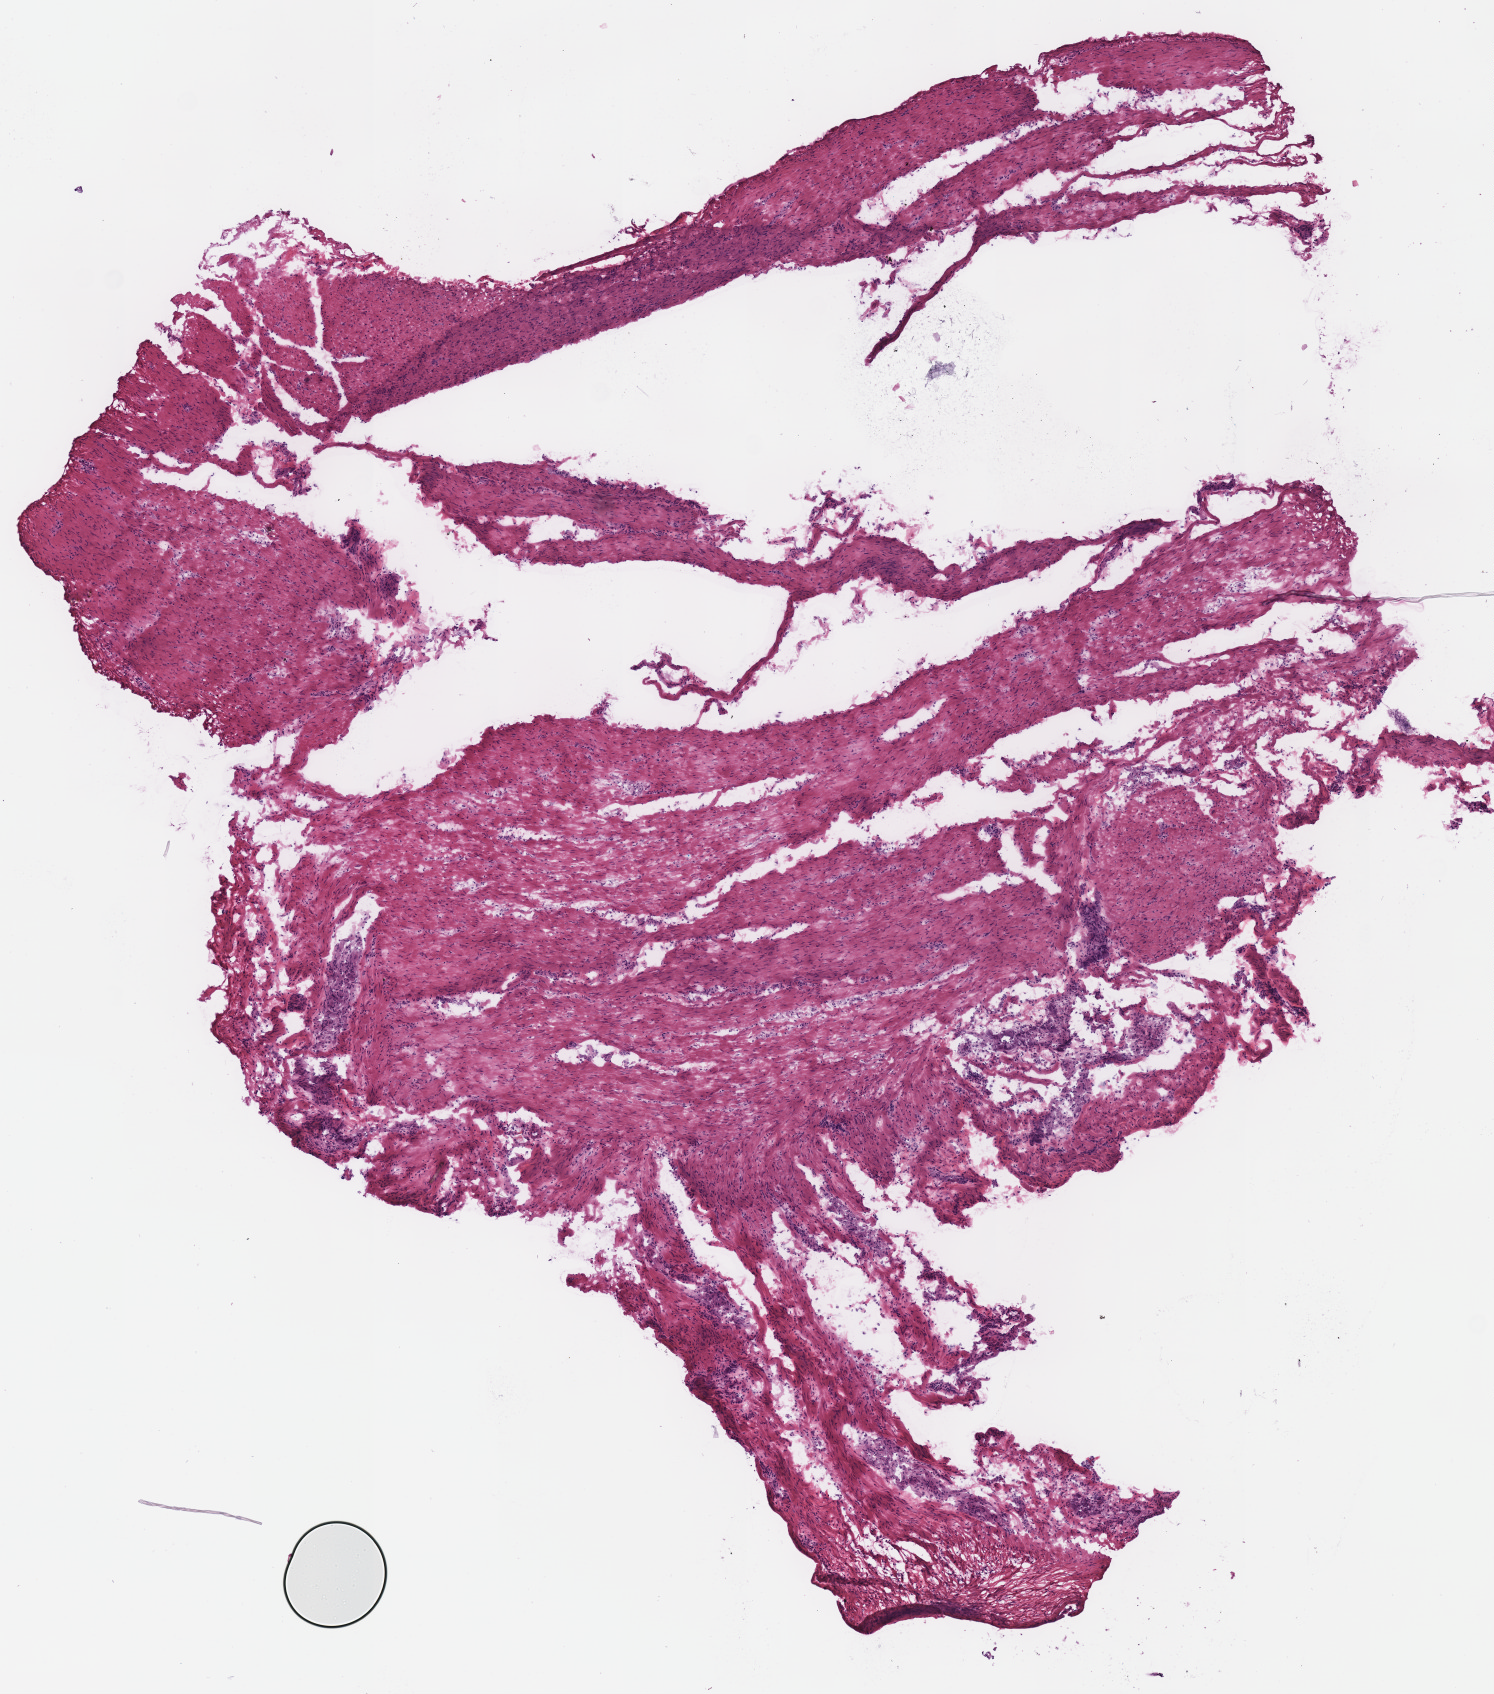
Hematoxylin and eosin (H&E) stained whole-slide image — low-resolution overview of the scanned area, about 5.9 x 6.7 mm (acquisition: 40x scan), frozen section from the top of the tissue portion, solid tissue normal (non-tumour tissue) sample from the stomach. Patient: male, age at initial diagnosis 75 years.
This section: solid tissue normal sample (biorepository sample class). Patient diagnosis: Tubular adenocarcinoma (body of stomach).